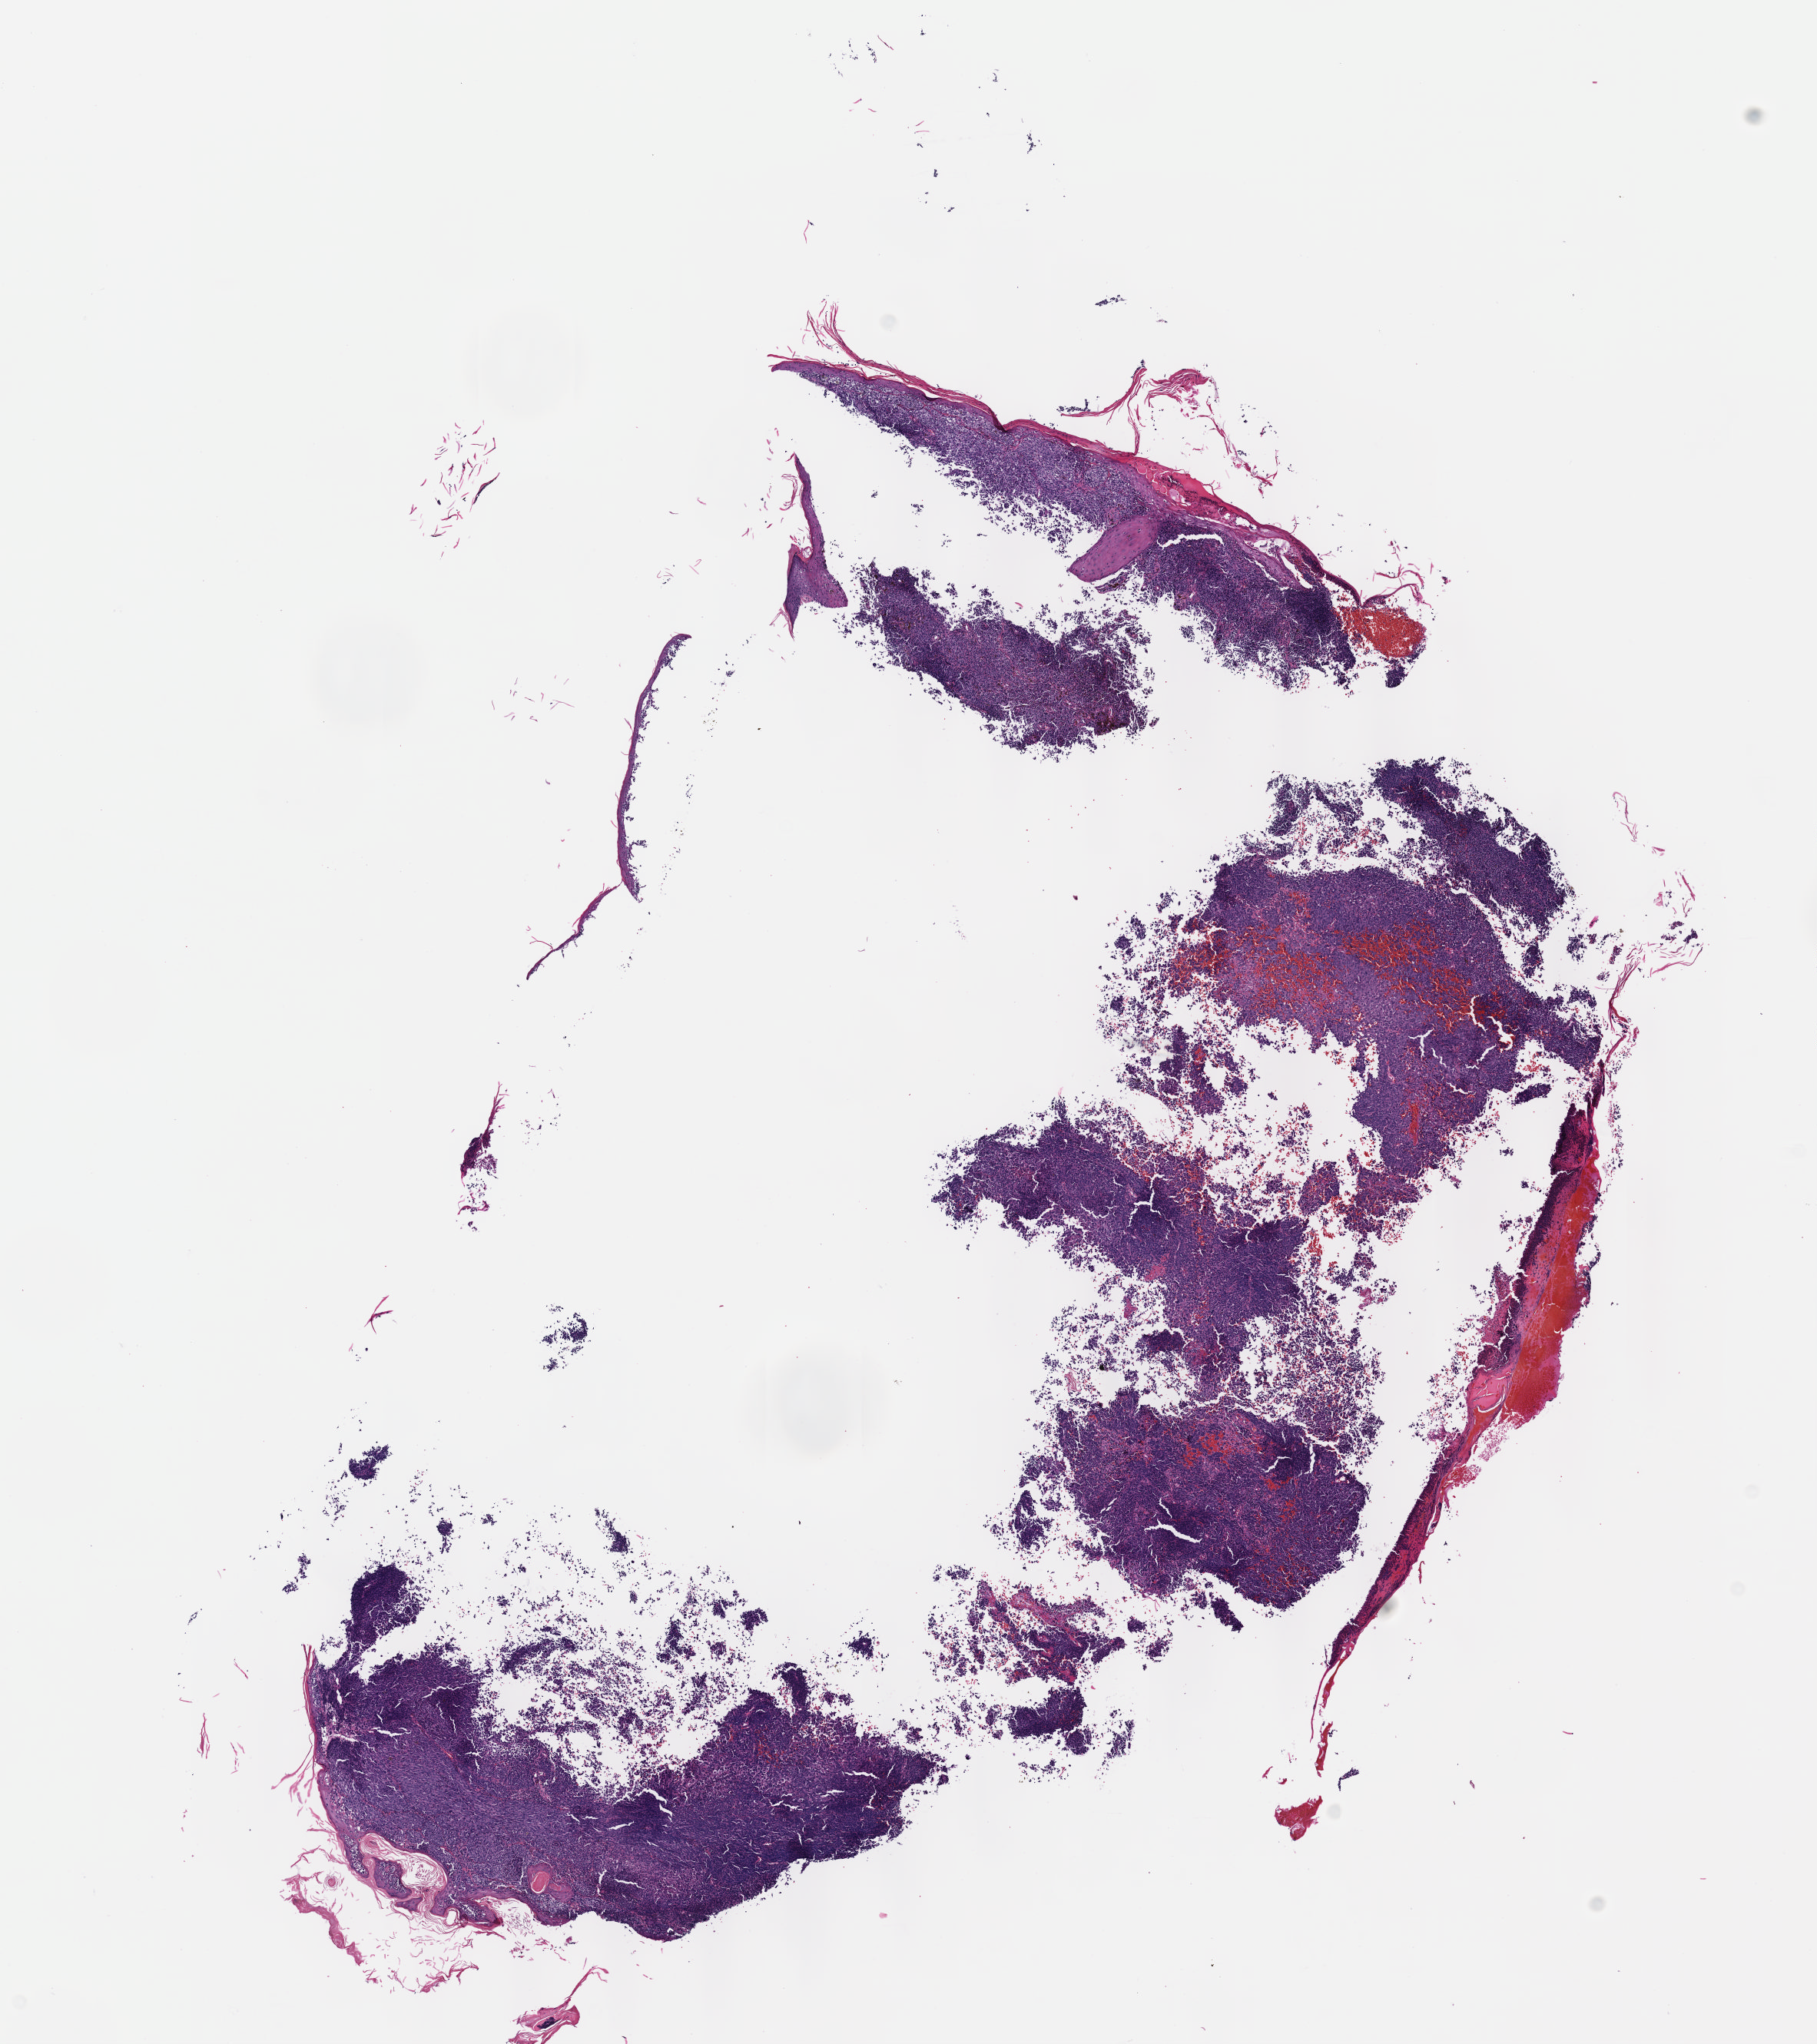
Digitized H&E-stained tissue section (whole slide), low-resolution overview of the scanned area, about 9.6 x 10.8 mm (slide scanned at 40x). FFPE section. Skin, primary tumour sample. Male, age 62 years at initial diagnosis.
Pathologic diagnosis: Epithelioid cell melanoma. AJCC pathologic stage: IIB (7th edition).